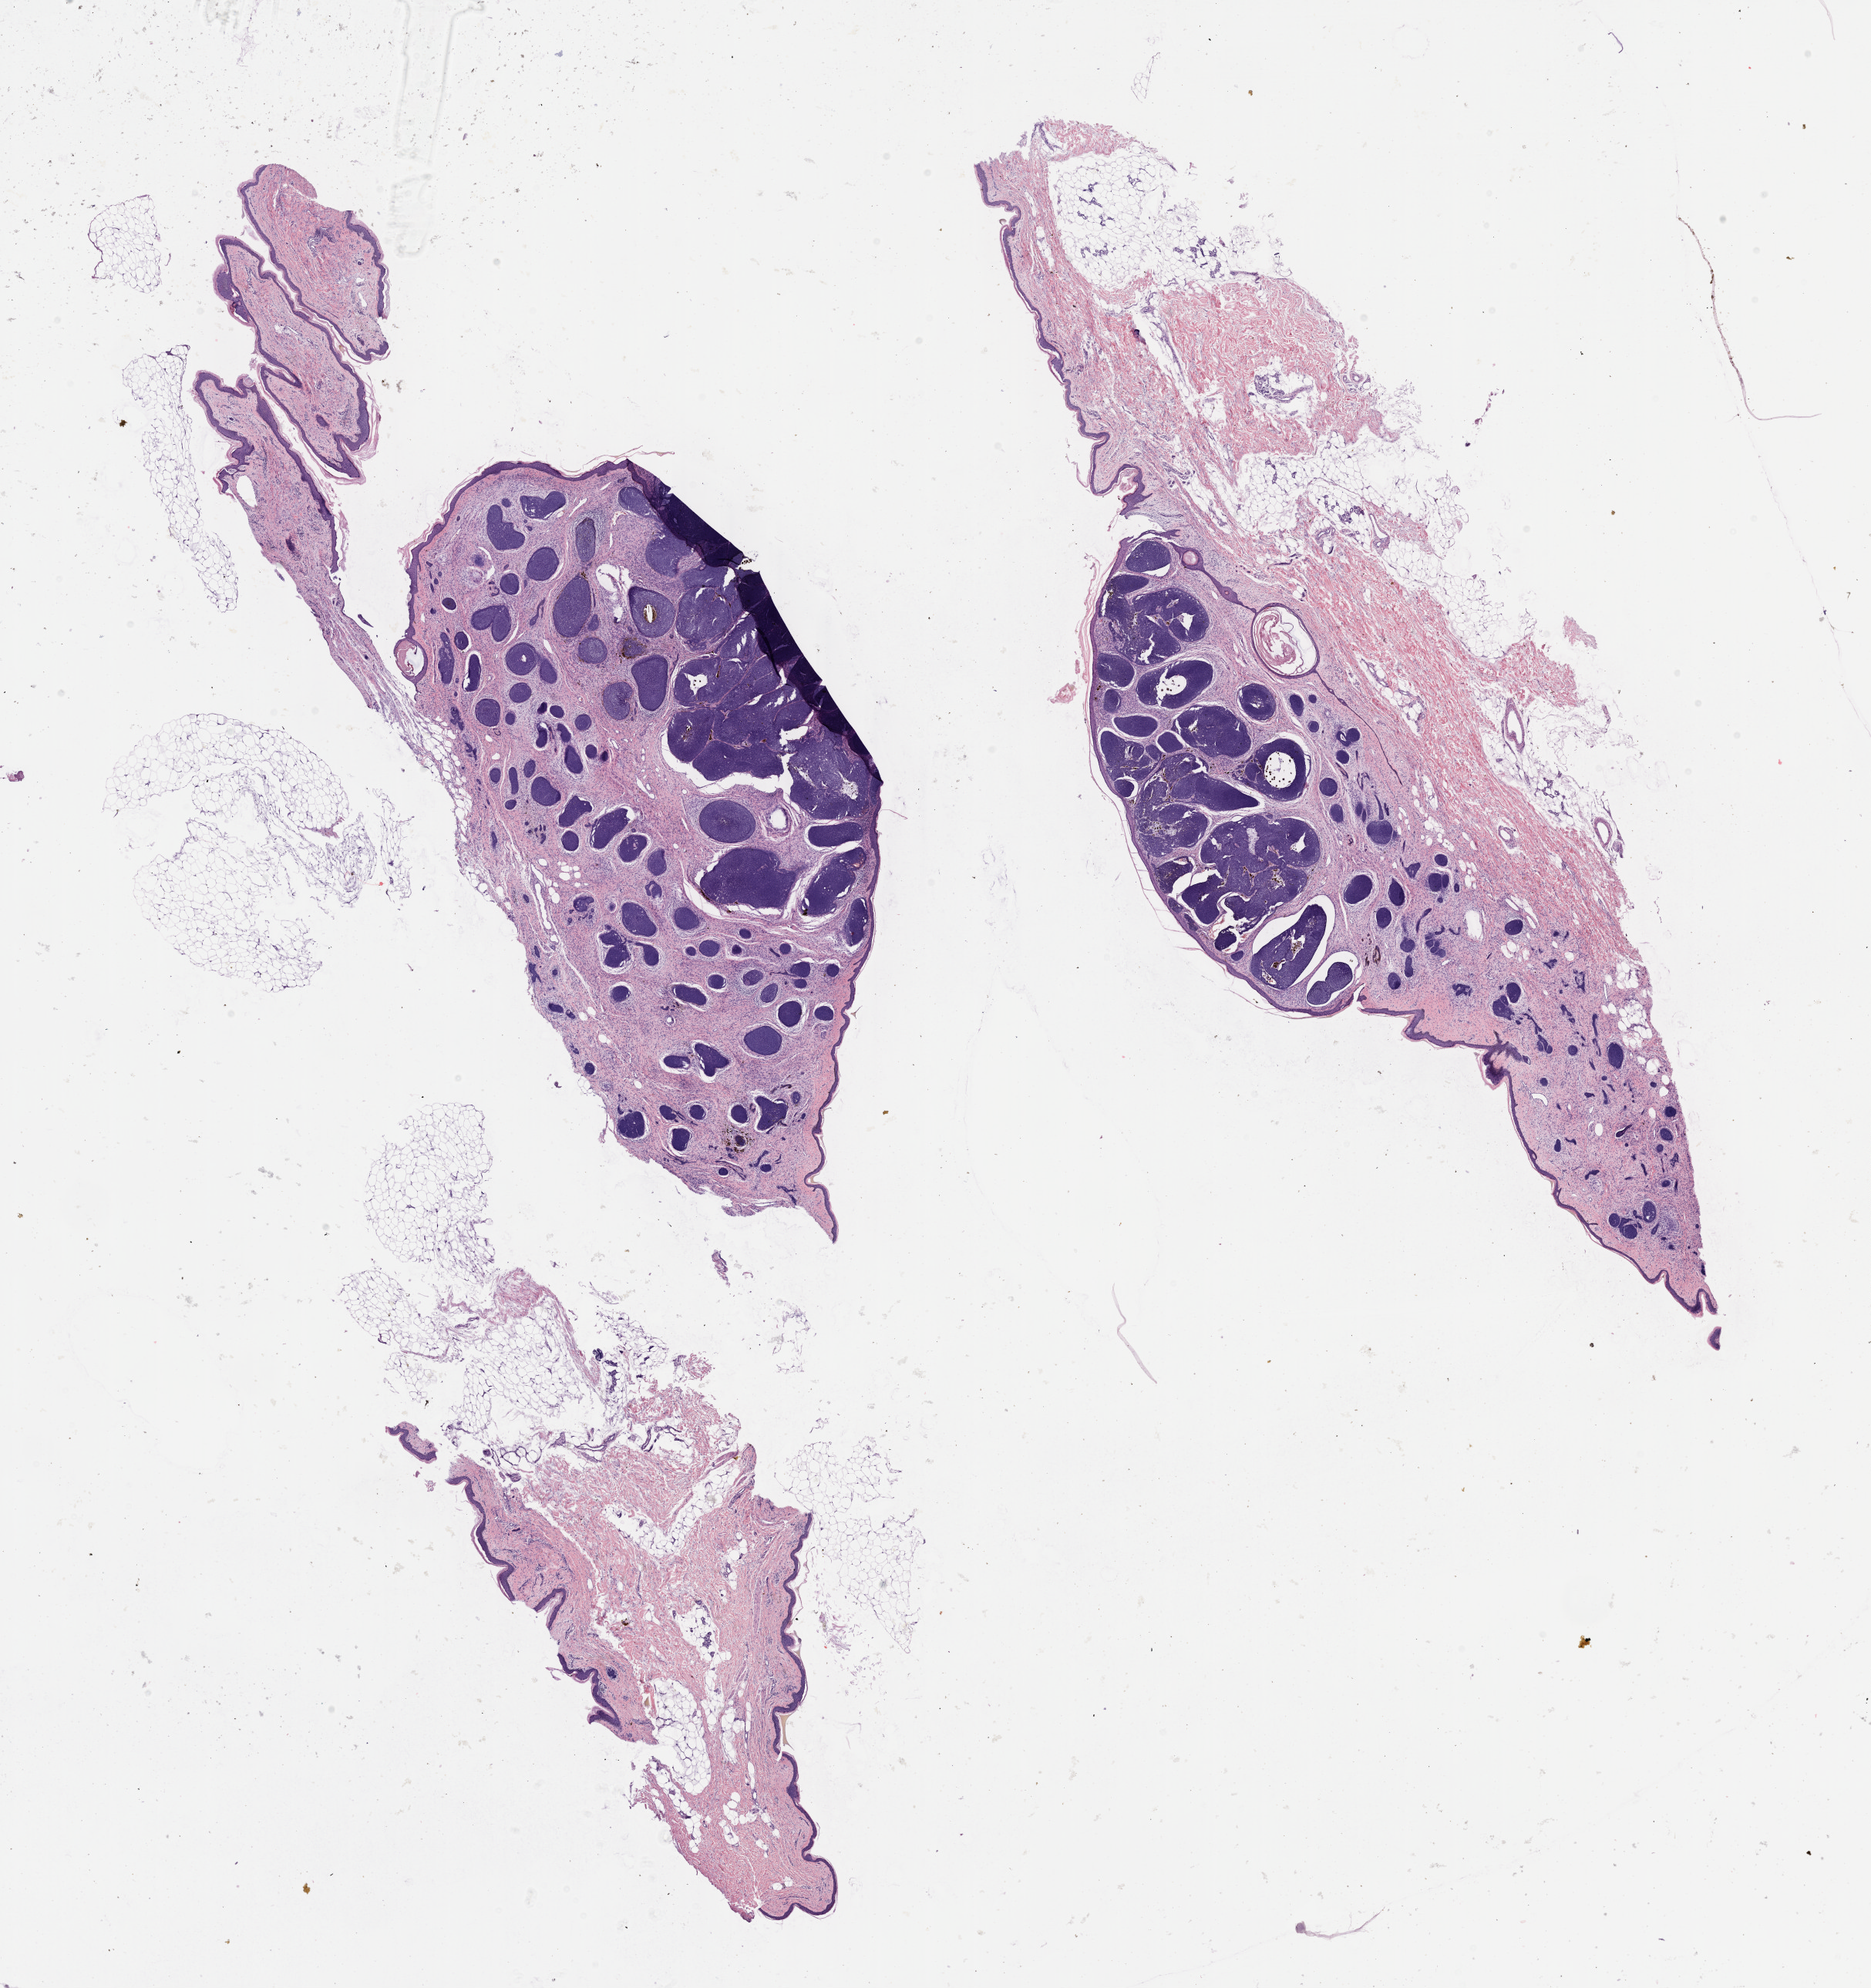
Digitized H&E tissue section (whole slide), shown as a low-resolution overview of the whole scanned area (about 19.6 x 20.8 mm, acquisition: 40x scan); formalin-fixed paraffin-embedded (FFPE) diagnostic section; primary tumour sample from the skin. Patient sex: female.
• diagnosis: Malignant melanoma, NOS
• TNM: T4 N0 M0
• AJCC pathologic stage: II (7th edition)